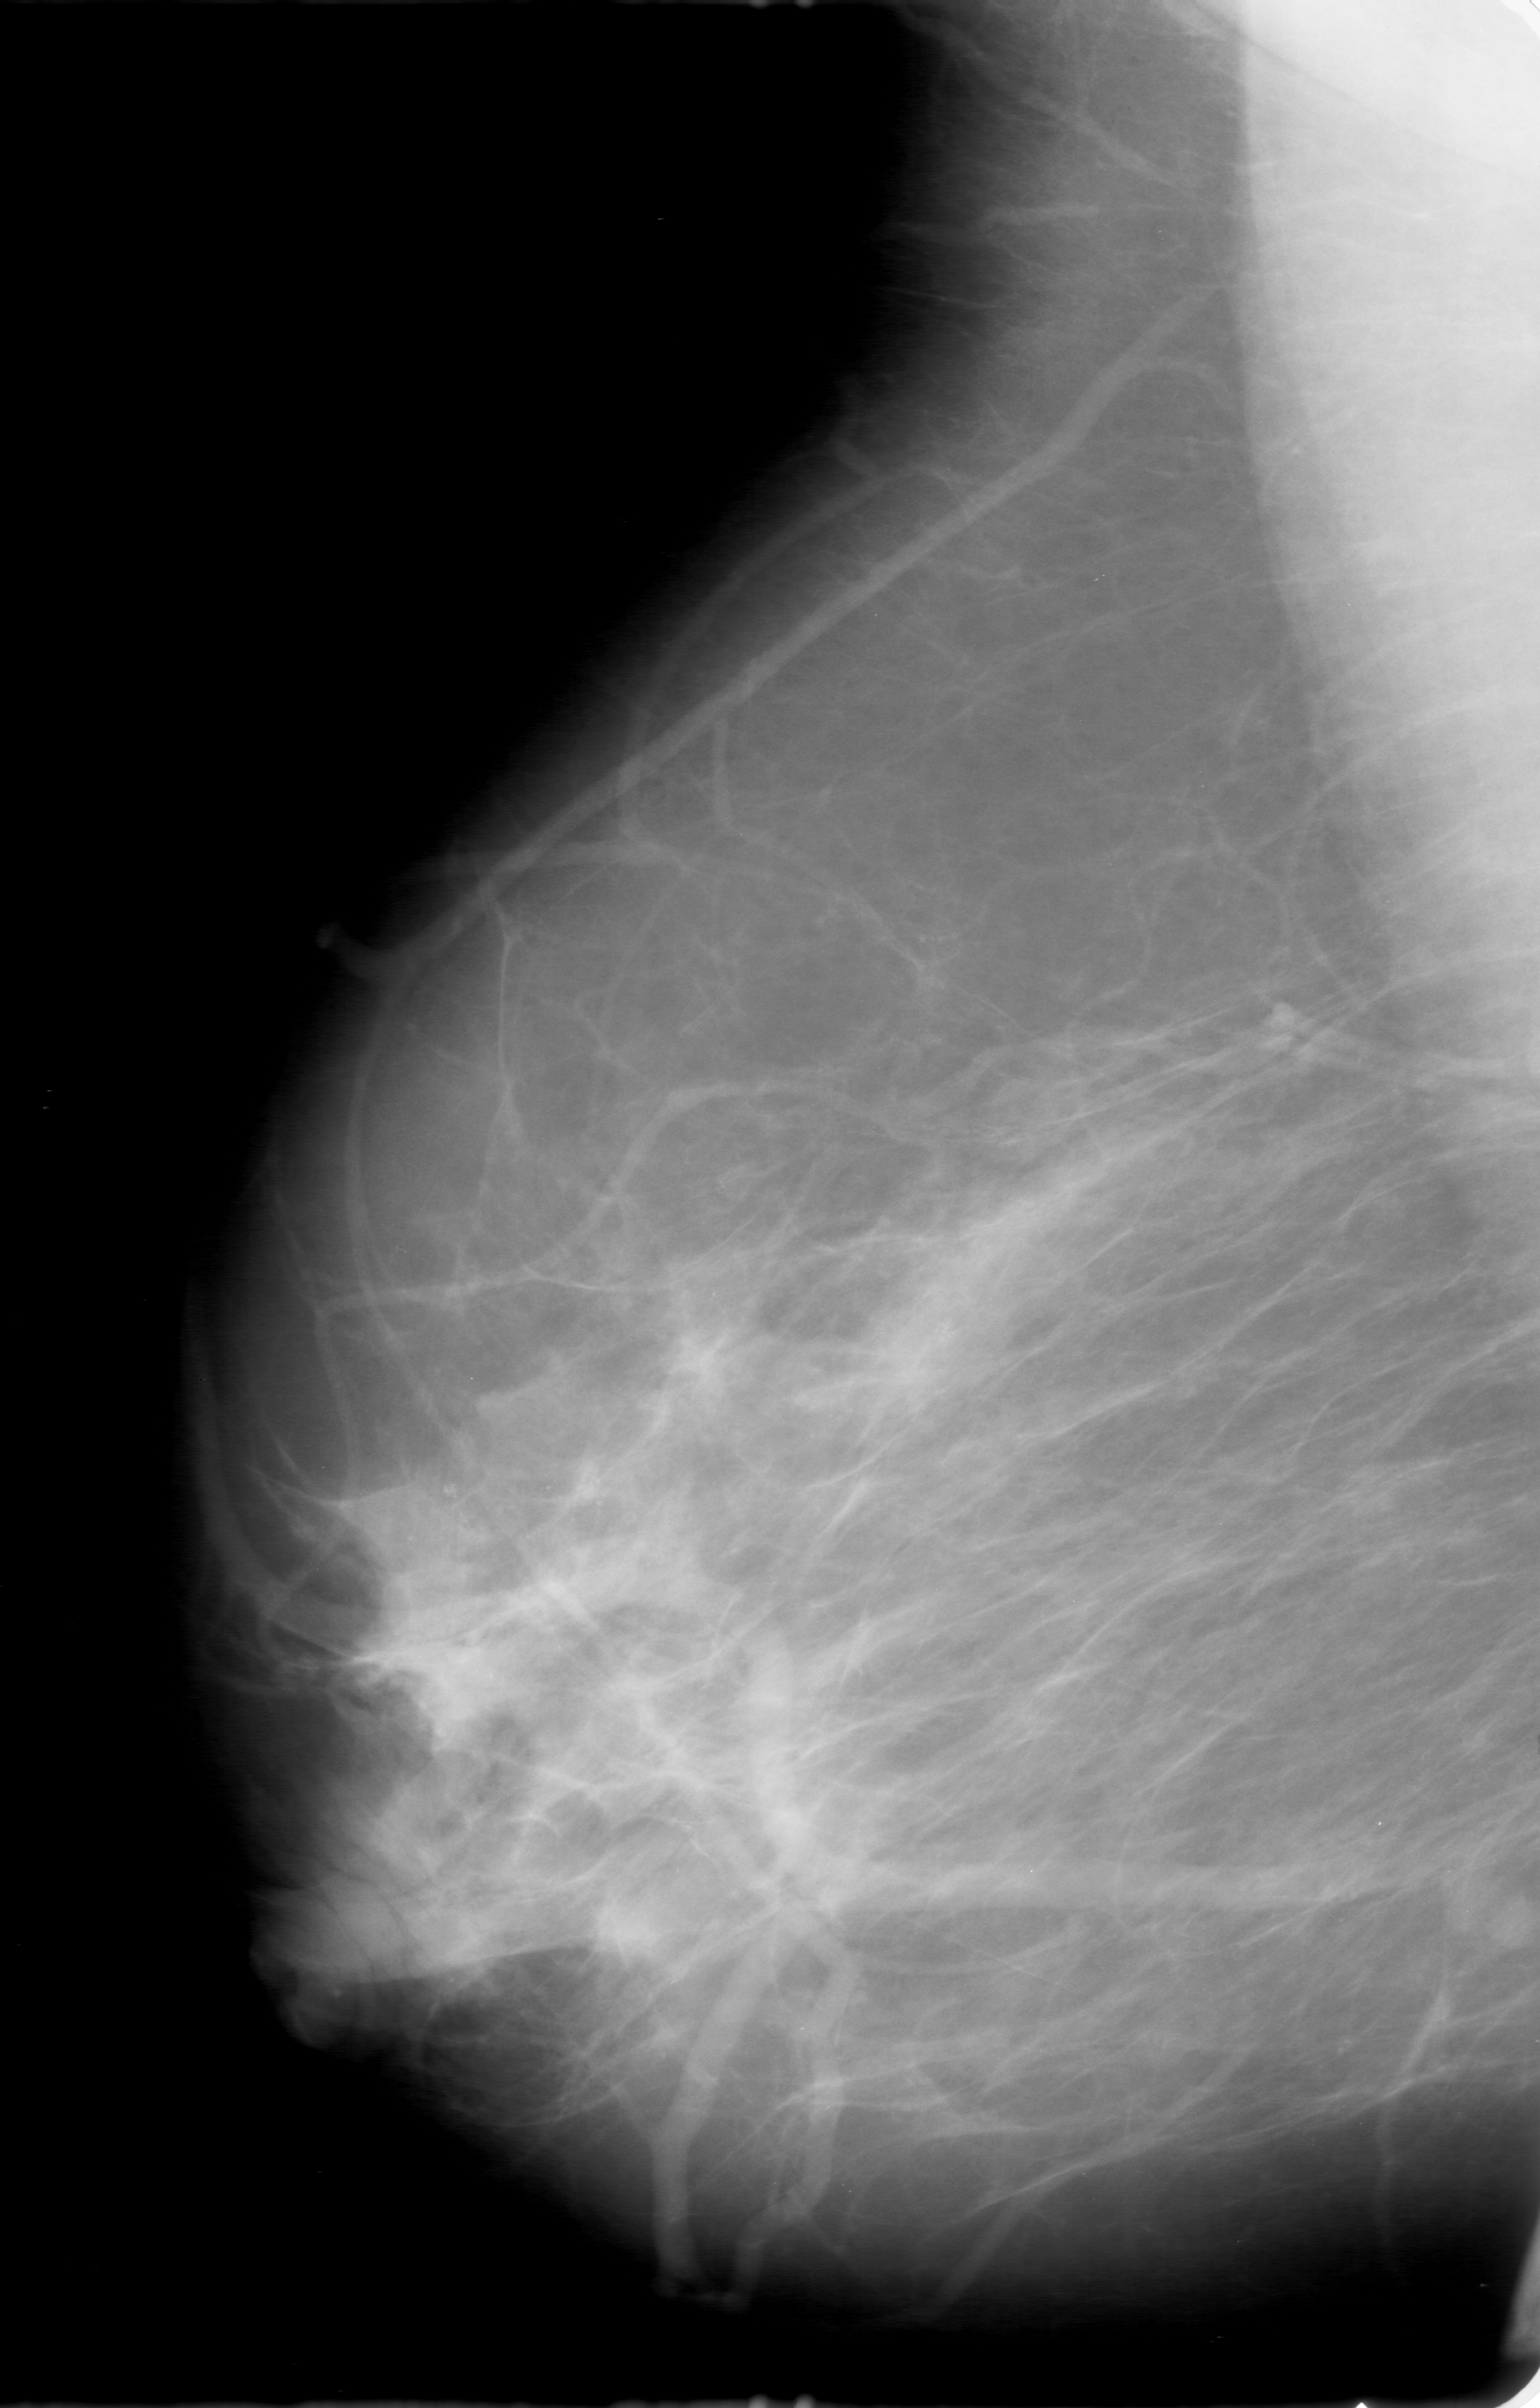
Digitized screen-film mammogram, right breast, MLO view, breast composition: scattered fibroglandular densities (BI-RADS density category 2 of 4).
- Abnormality record for this image: calcifications, morphology amorphous, distribution segmental; BI-RADS assessment category 0; subtlety rating 3 on a 1 (subtle) to 5 (obvious) scale; pathology result (as recorded, not read from the image): malignant.